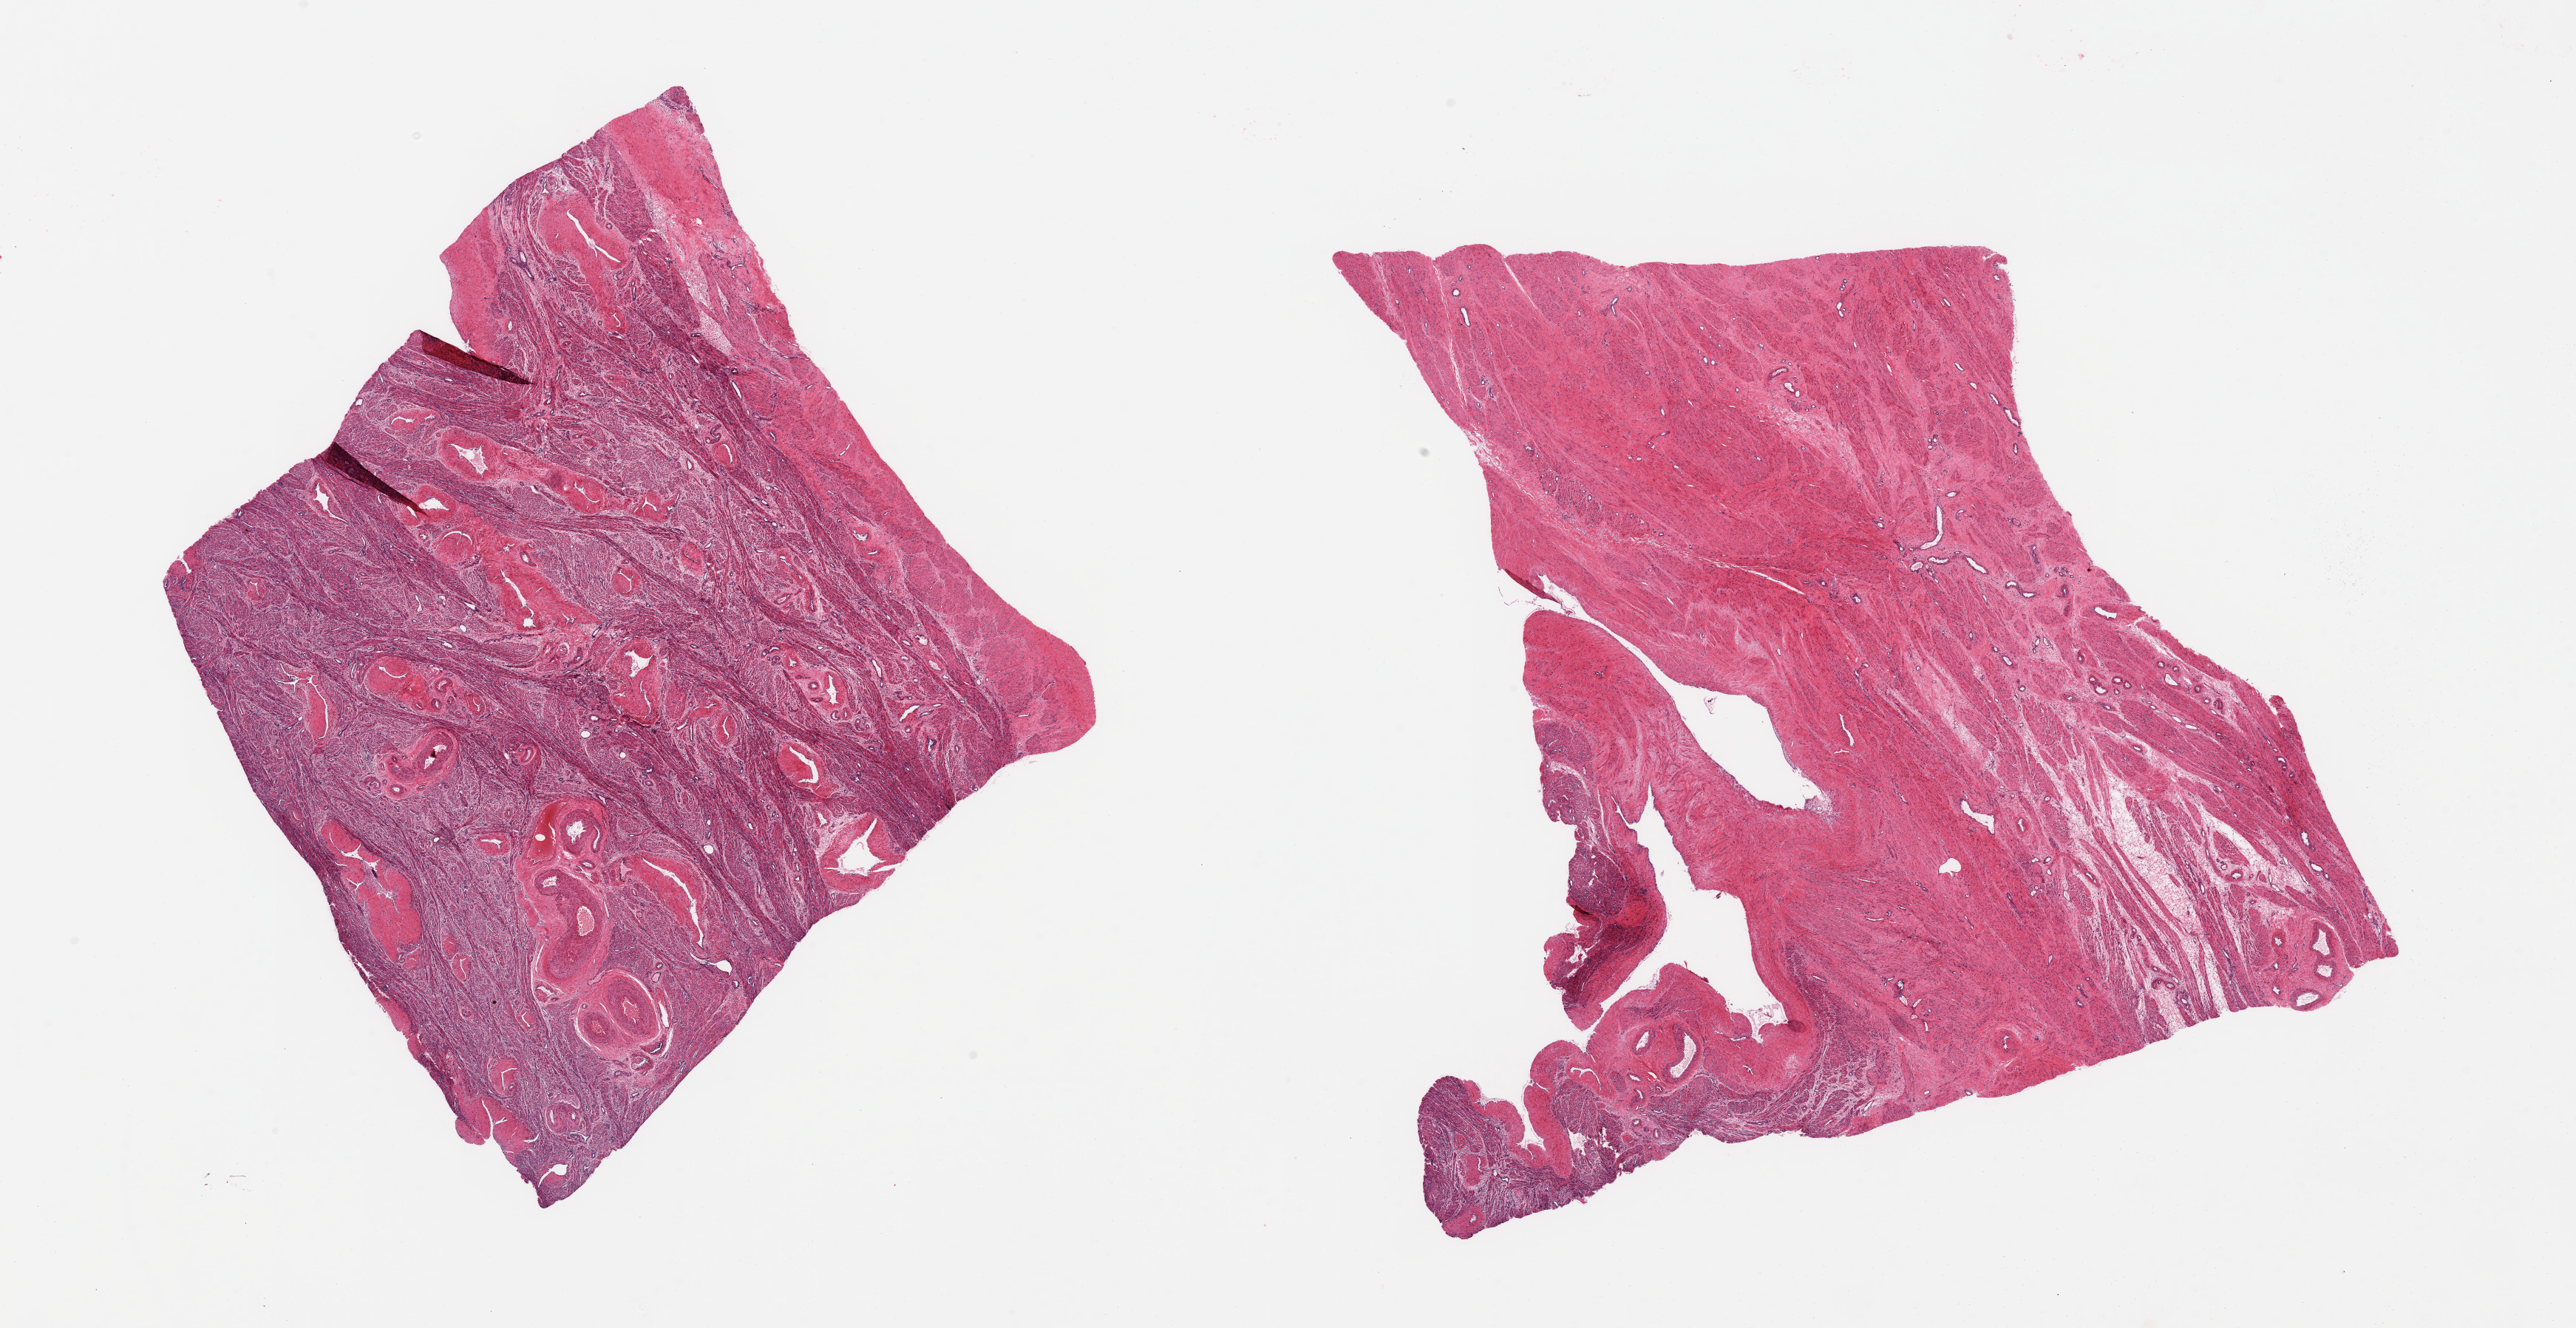
H&E whole-slide image, brightfield — whole scanned area (about 27.6 x 14.2 mm, acquisition: 20x scan) shown as a low-resolution overview. PAXgene-fixed paraffin-embedded (PFPE) section. Section of uterus (target tissue). Donor tissue sample. Donor: female.
Reviewer comment on this tissue sample: 2 pieces; mostly parametrium with prominent thick walled vessels; no target endometrium or myometrium present.